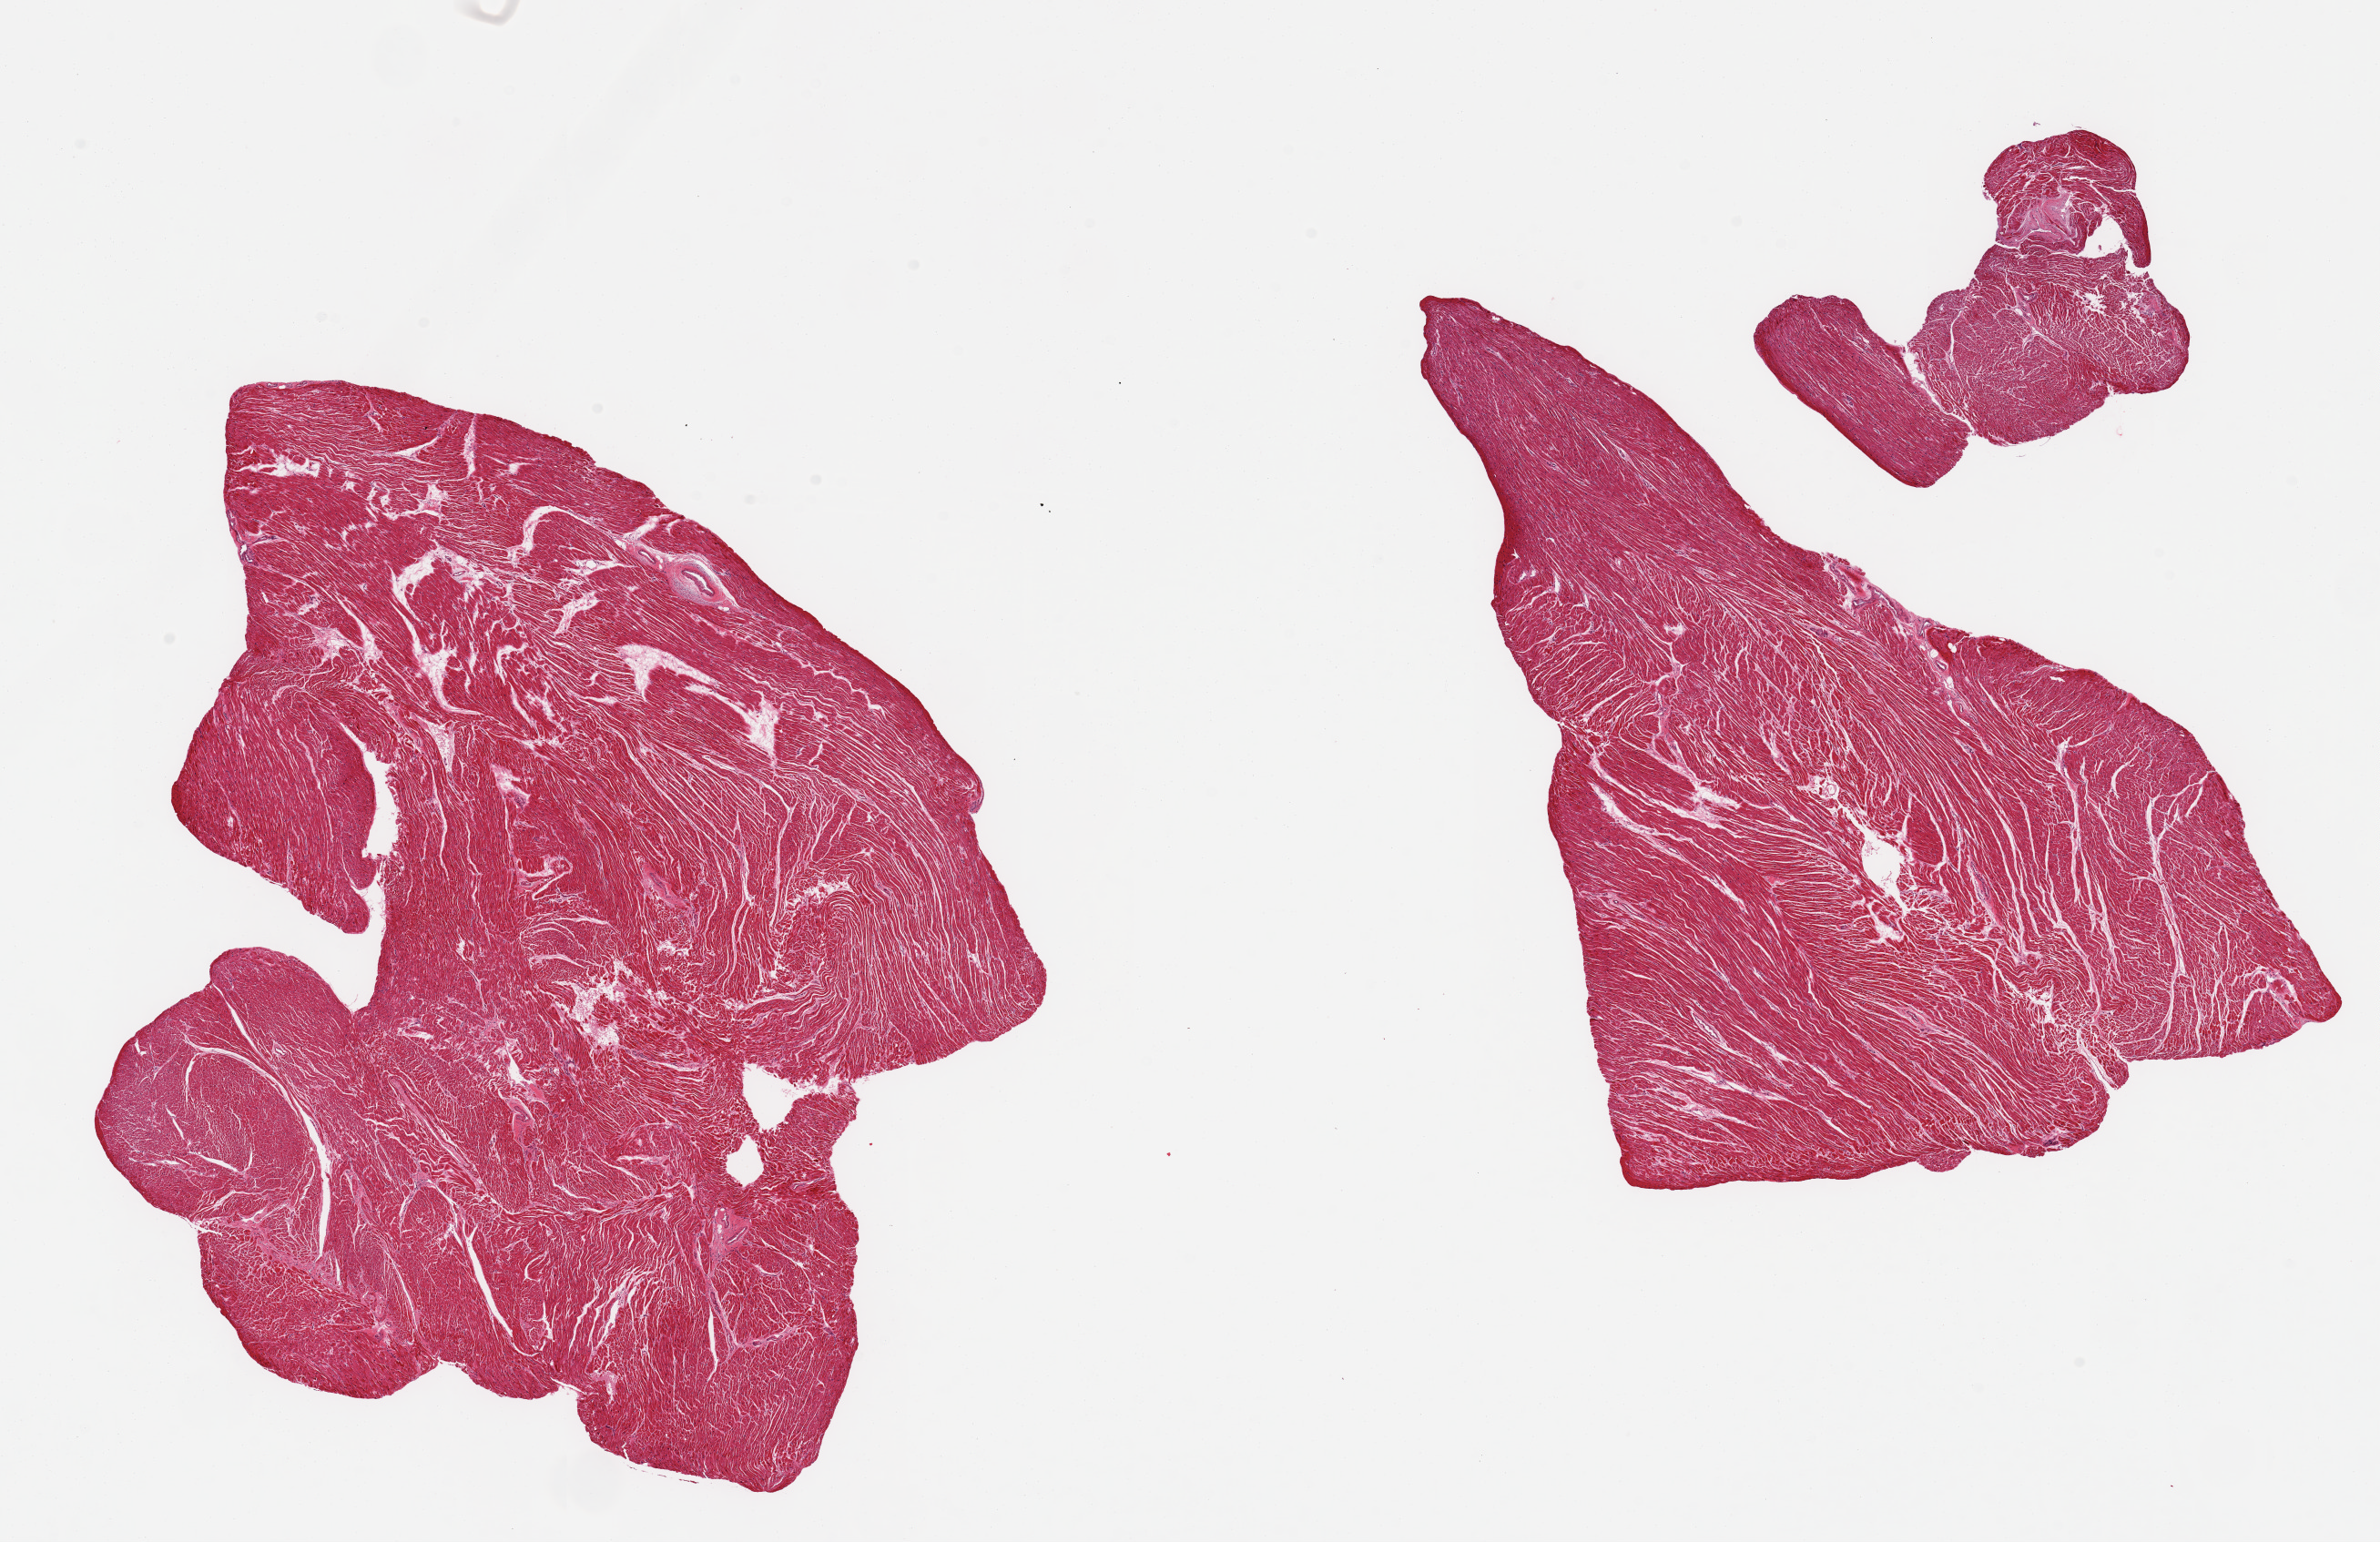
Digitized haematoxylin and eosin-stained section, brightfield — shown as a low-resolution overview of the whole scanned area (about 20.7 x 13.4 mm); PAXgene-fixed paraffin-embedded (PFPE) section; target tissue: heart; donor tissue sample. Donor sex: male.
• reviewer comment on this tissue sample: 2 pieces; focal interstitial fibrosis; autolyzed fatty degeneration